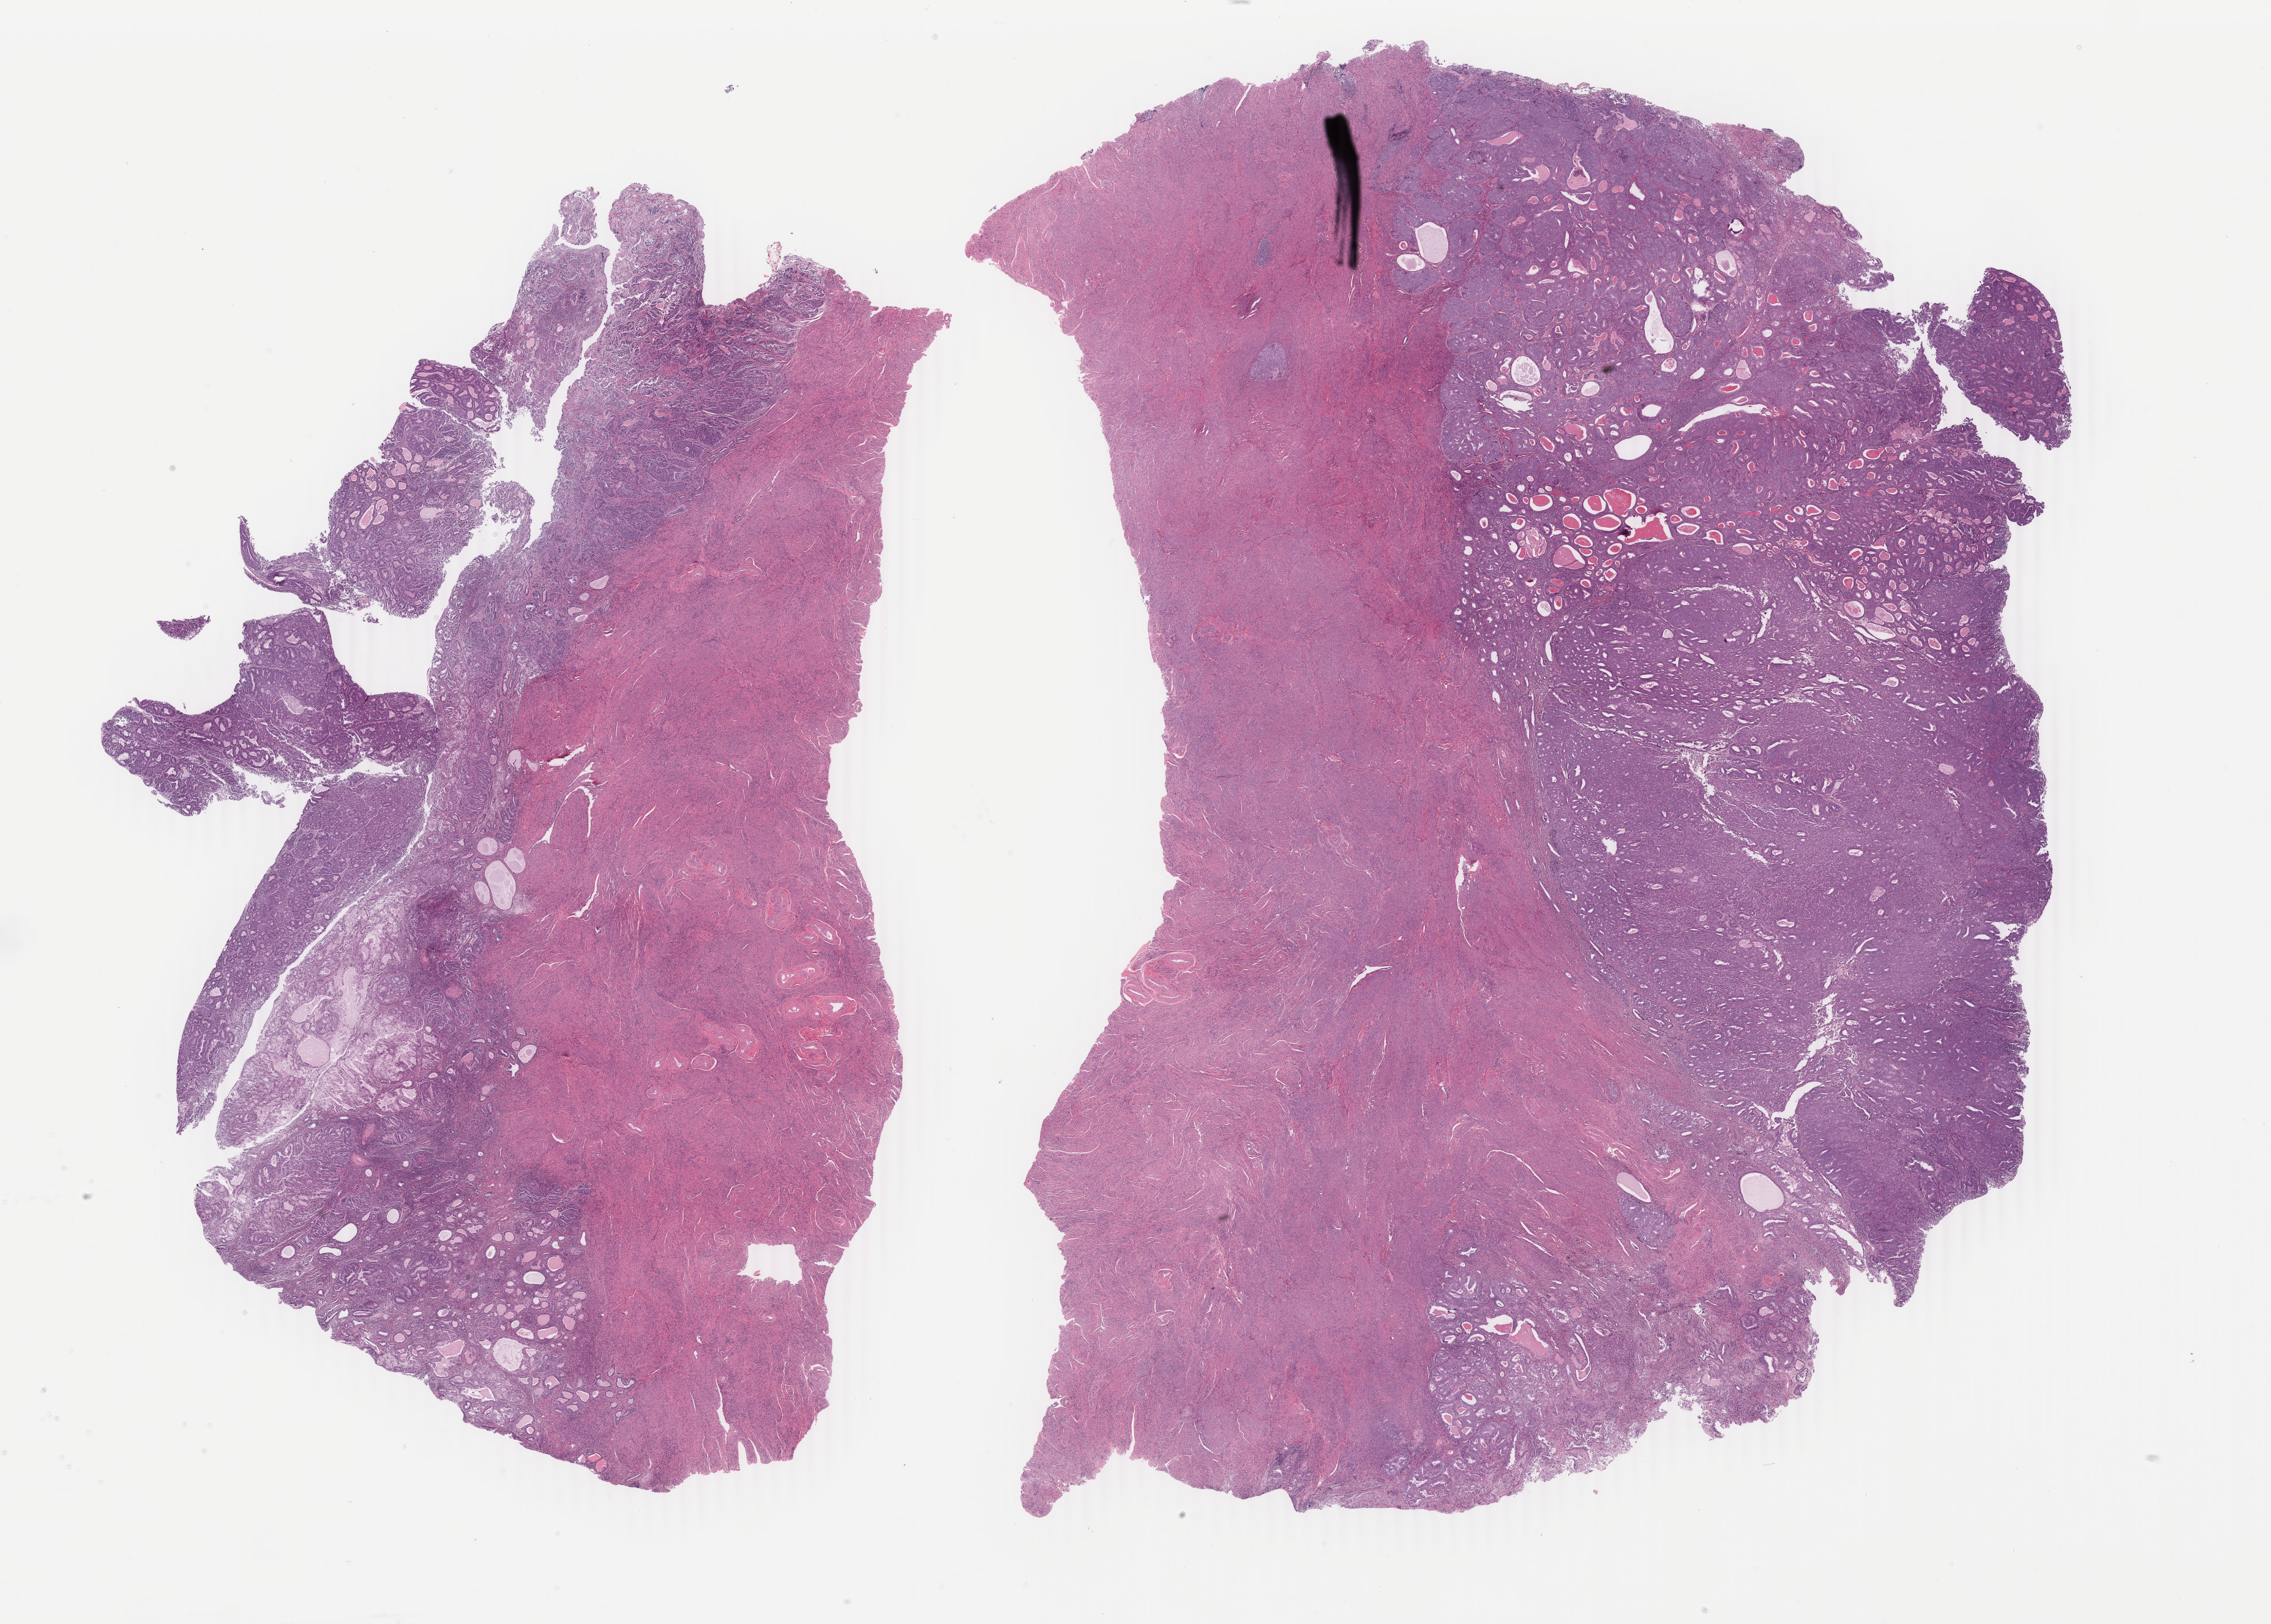
Whole-slide histology image, H&E-stained — a low-resolution overview of the entire scanned area, about 29.5 x 21.1 mm (from a 40x scan). Formalin-fixed paraffin-embedded (FFPE) diagnostic section. Sample: primary tumour, uterus. Patient: female, age at initial diagnosis 67 years. Histologic grade: G2 (moderately differentiated).
• diagnosis: Endometrioid adenocarcinoma, NOS (endometrium)
• FIGO stage: IB